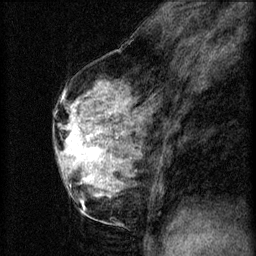
Breast MRI (dynamic contrast-enhanced), one sagittal slice; slice 35 of 60 in the series (ordered by position); 3 images stored at this slice position (order not interpretable as contrast timing); 1.5 T; TE 4.2 ms, TR 8.2 ms; 256 × 256 image matrix, field of view 180 × 180 mm. Patient: female, 56 years.
Structures marked on this image (semi-automatic segmentation, software-assisted and operator-edited):
- analysis volume of interest (the breast-tissue region the enhancement analysis was run in; not a lesion): bounding box (x1, y1, x2, y2) in pixels: (60, 124, 114, 179)
- tumour enhancement mask (voxels above the 70 % enhancement threshold inside the analysis volume of interest): (66, 124, 101, 179)